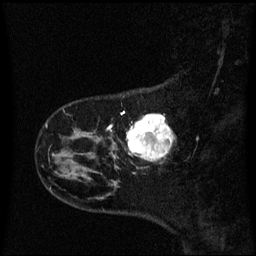
Breast MRI (dynamic contrast-enhanced), one sagittal slice; slice 12 of 60 in the series (ordered by position); dynamic contrast-enhanced series, image 2 of 3 at this slice position (ordered by acquisition); 1.5 T; TE 4.2 ms, TR 8.4 ms; 2 mm slice thickness; 256 × 256 image matrix. Female patient, age 41 years. From the clinical record (not read from this slice): setting: breast cancer imaged before/during neoadjuvant chemotherapy; receptor status: triple-negative.
Structures marked on this image (semi-automatically segmented with operator editing):
- analysis volume of interest (the breast-tissue region the enhancement analysis was run in; not a lesion): bounding box <116,112,173,169> (left, top, right, bottom; pixels)
- tumour enhancement mask (voxels above the 70 % enhancement threshold inside the analysis volume of interest): <127,114,173,159>